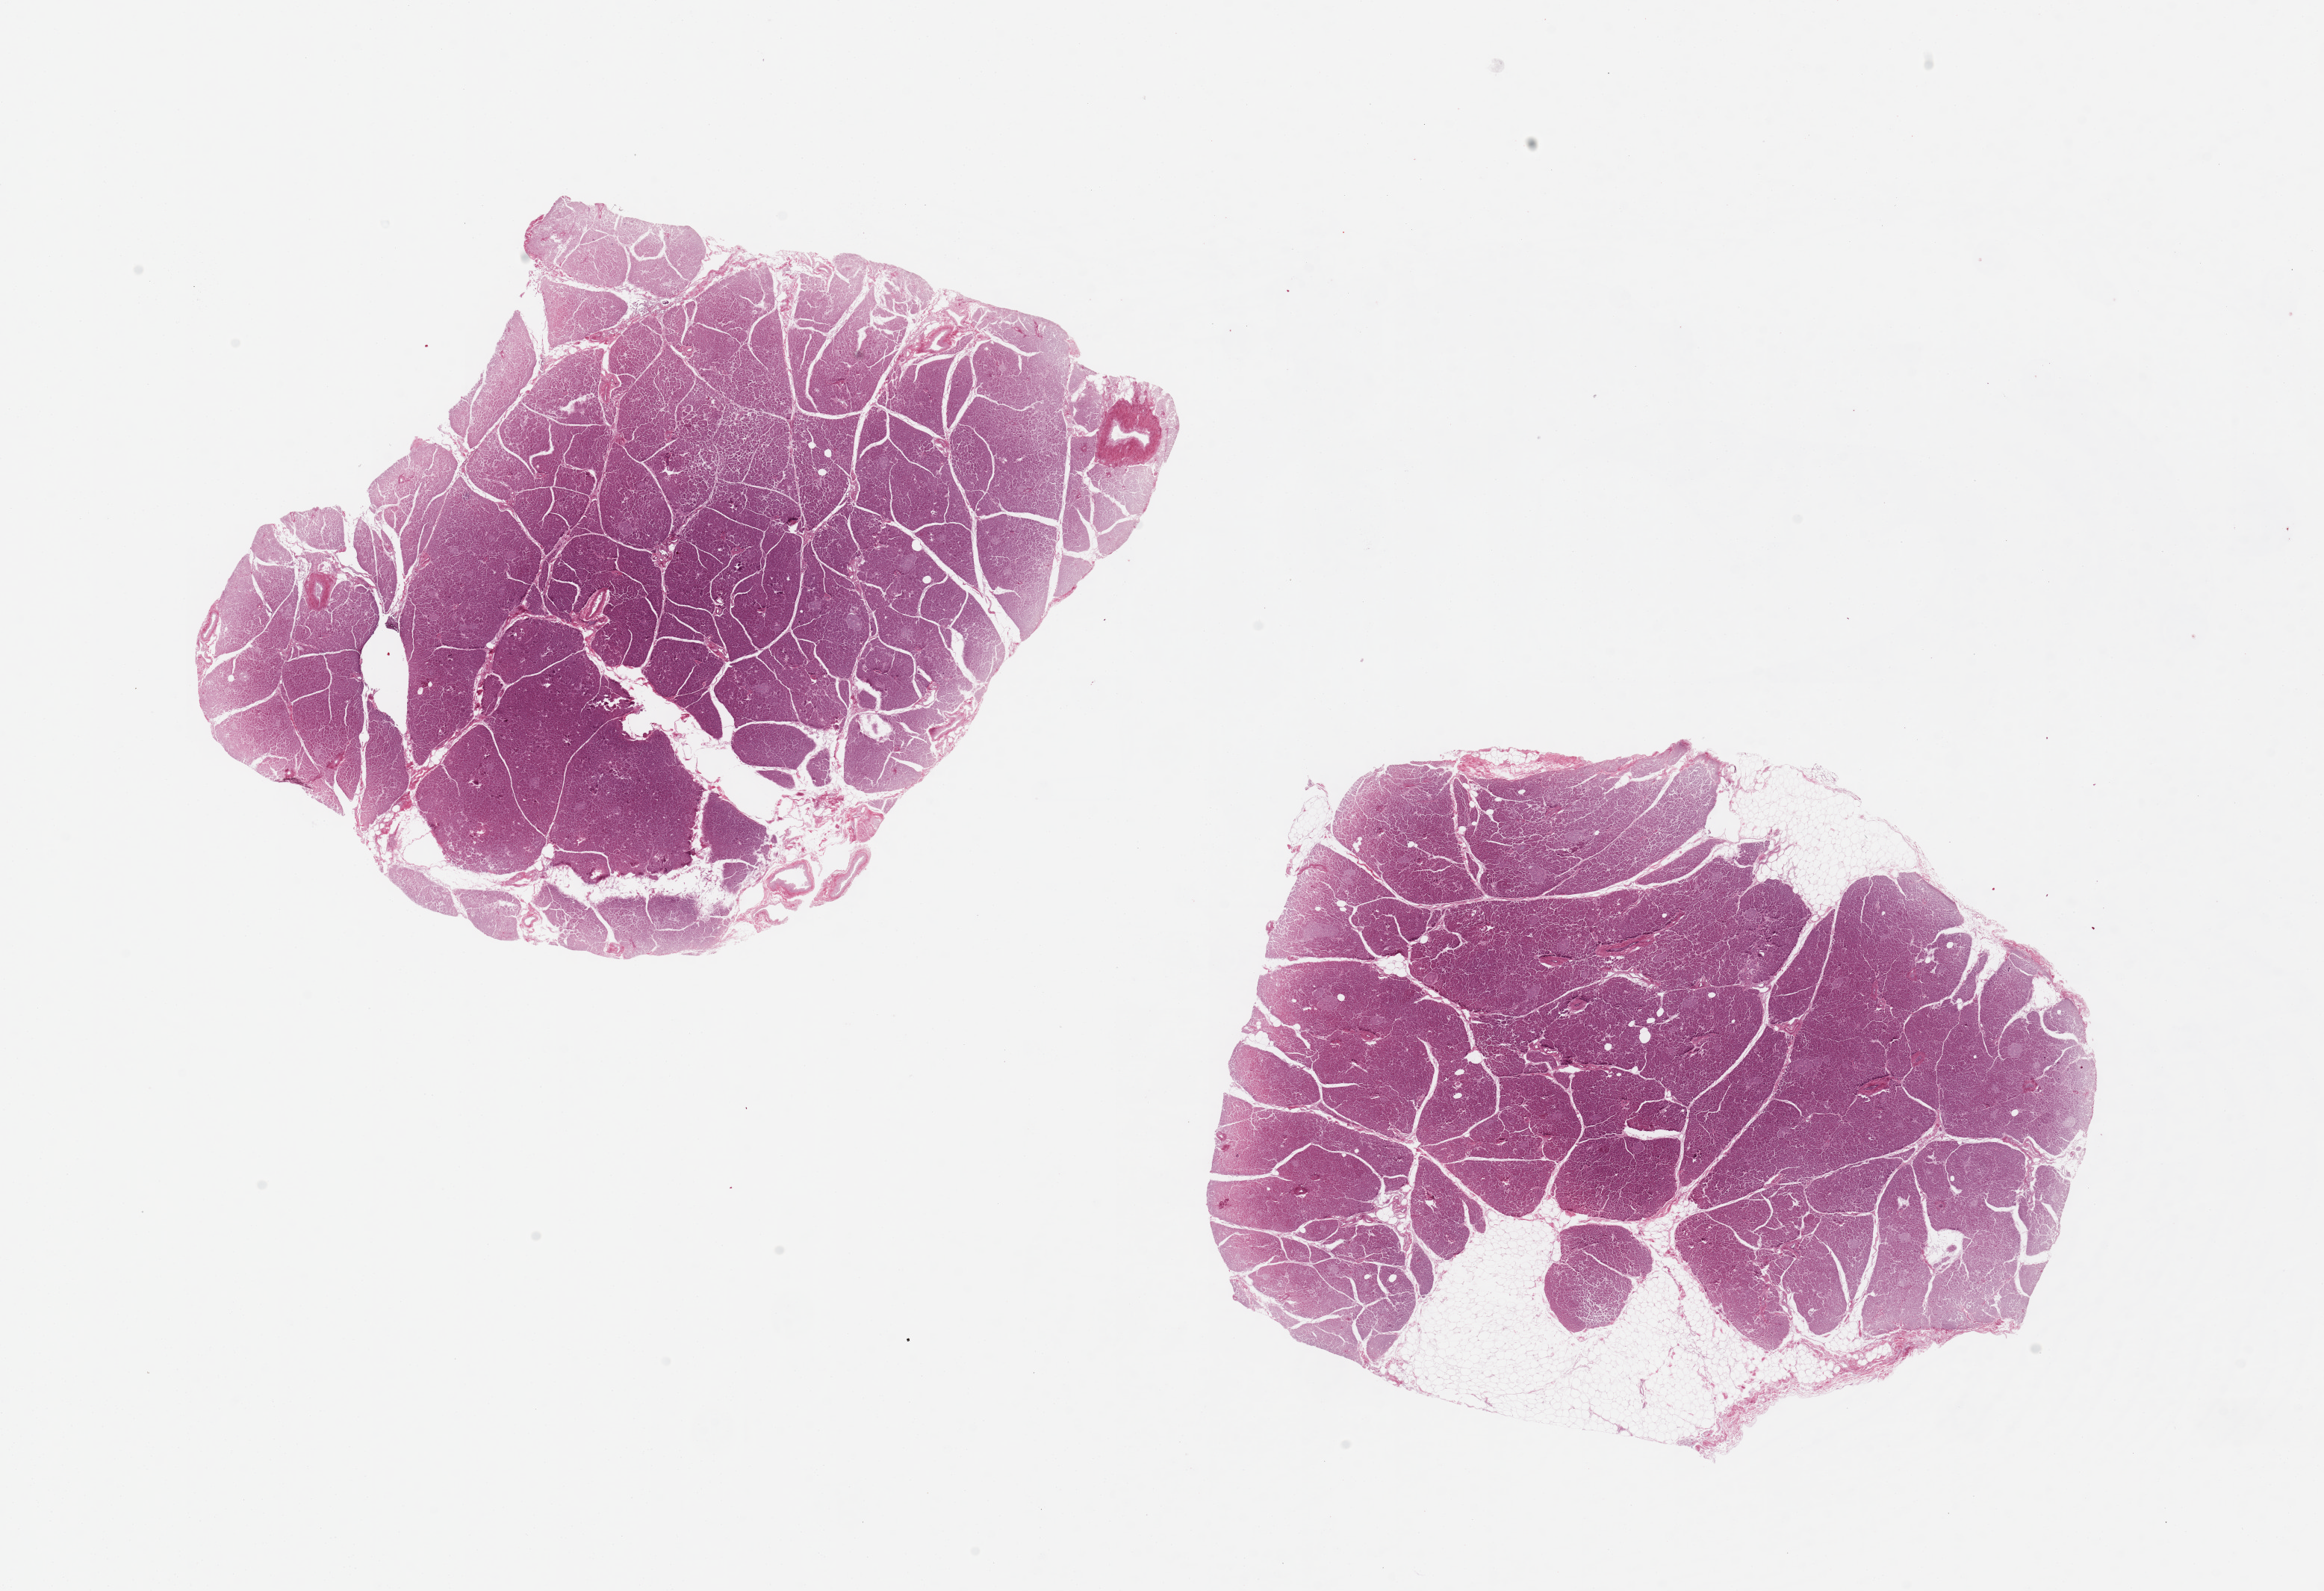
Hematoxylin and eosin (H&E) whole-slide image, brightfield, low-resolution overview of the scanned area, about 24.6 x 16.8 mm; PAXgene-fixed, paraffin-embedded tissue; sampled site (target tissue): pancreas; tissue donor sample.
- reviewer comment on this tissue sample: 2 pieces 10x9mm. Badly autolyzed with saponification. Islets discernable but totally autolyzed